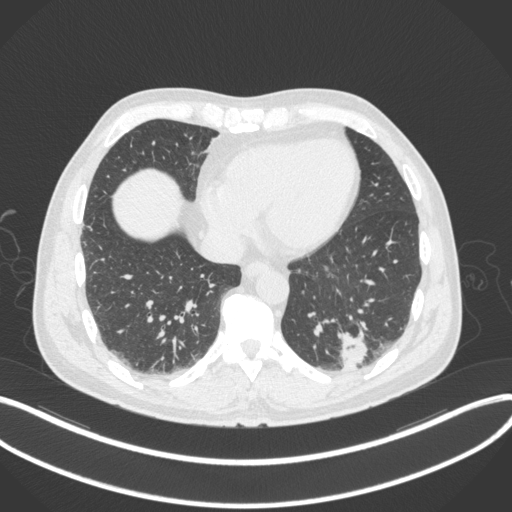
Chest CT, one axial slice. Position 84 of 313 along the scan axis. Reconstruction kernel B31f. 120 kVp. Lung window (W 1500 / L -600 HU). 512 × 512 image matrix, field of view 400 × 400 mm. Male patient, age 54 years. Case-level facts recorded for this patient, not image findings: clinical TNM (as recorded): T1c N0 M1.
Structures marked on this image (bounding box drawn by a radiologist):
- lung tumour (recorded histology: adenocarcinoma): bounding box (x1, y1, x2, y2) in pixels: (330, 325, 366, 372)